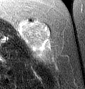
MRI of an extremity soft-tissue mass, one axial slice. Slice 25 of 46 in the series (ordered by position). T2-weighted fat-saturated. MR volume resampled by the dataset authors to the PET/CT grid (not the native acquisition matrix). 3.27 mm slice thickness. 85 × 89 image matrix, field of view 83 × 87 mm. Female patient. From the clinical record (not read from this slice): histological type: leiomyosarcoma; grade: intermediate; site of the primary tumour: parascapusular.
Outlined on this slice (expert contour drawn on MRI and transferred to this co-registered scan by the dataset authors):
- gross tumour volume including surrounding oedema: bounding box <18,19,53,58> (left, top, right, bottom; pixels)
- gross tumour volume (mass): <22,19,51,51>